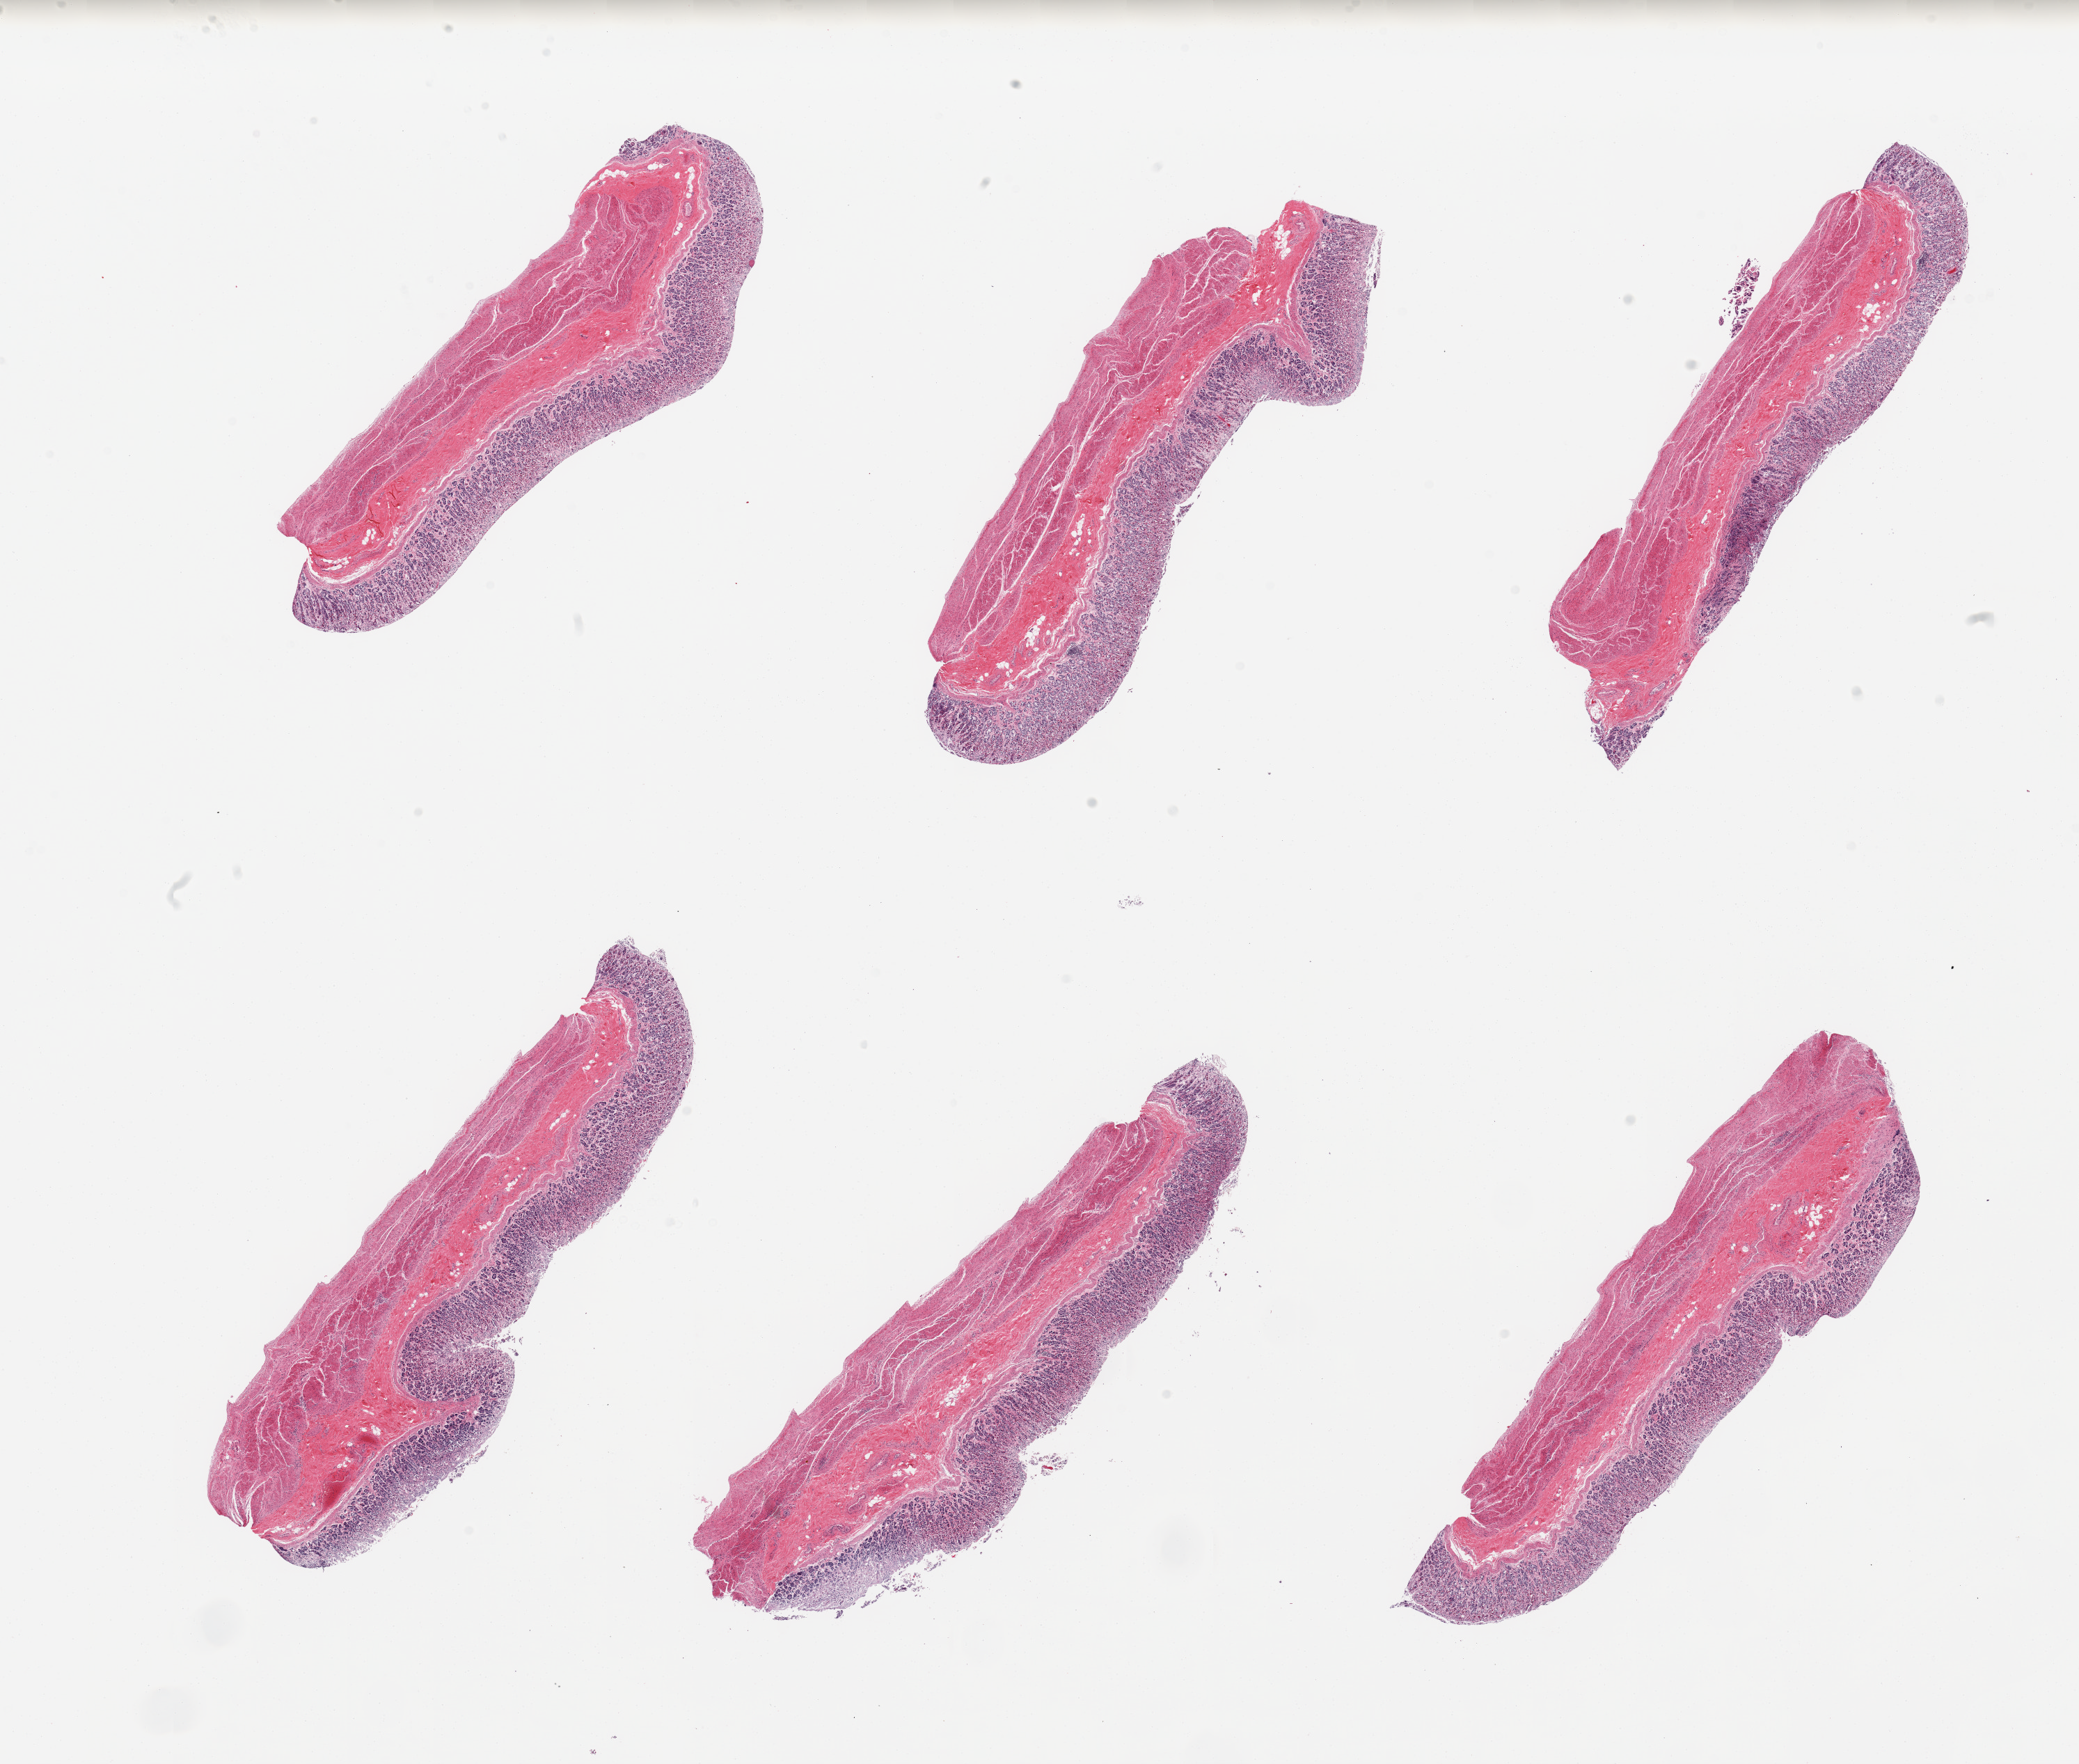
Hematoxylin and eosin (H&E) whole-slide image, brightfield, whole scanned area (about 23.6 x 20.0 mm) shown as a low-resolution overview. PAXgene-fixed, paraffin-embedded tissue. Sampled site (target tissue): stomach. Tissue donor sample. Female donor.
Pathologist's review note for this sample: 6 pieces, mucosa is ~0.6mm, ~30-40% thickness, moderately autolyzed.